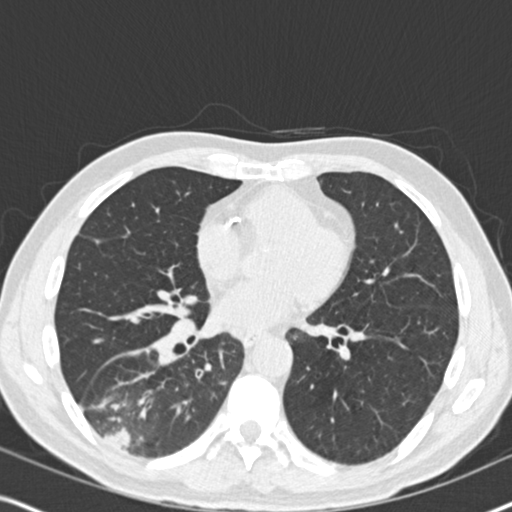
Low-dose screening chest CT, one axial slice. Slice 88 of 182 in the series (ordered by position). Reconstruction kernel B30f. Lung window (W 1500 / L -600 HU). 512 × 512 image matrix.
Outlined on this slice (outlined manually by an expert reader):
- lesion 1 (tumor, lower lobe of right lung): bounding box [x1, y1, x2, y2] px = [104, 428, 130, 448]